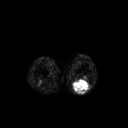
FDG PET of an extremity soft-tissue mass (from a PET/CT study), one axial slice; position 186 of 267 along the scan axis; 3.27 mm slice thickness; 128 × 128 image matrix. Patient: male, 54 years. From the clinical record (not read from this slice): histological type: synovial sarcoma; site of the primary tumour: left poplietal fossa.
Outlined on this slice (expert contour drawn on MRI and transferred to this co-registered scan by the dataset authors):
- gross tumour volume (mass): box from (x=72, y=78) to (x=91, y=93) px